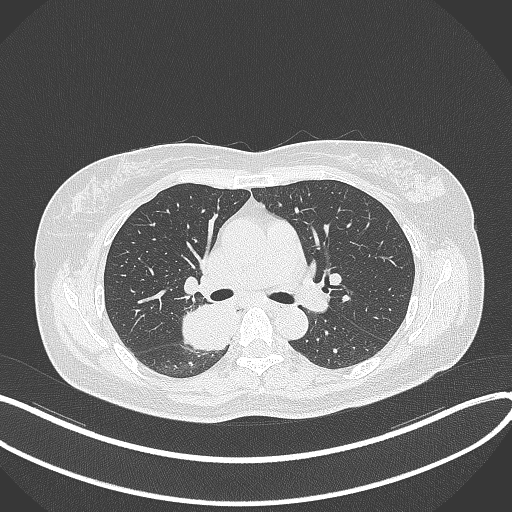
Chest CT, one axial slice; position 222 of 331 along the scan axis; lung window (W 1500 / L -600 HU); 1 mm slice thickness; 512 × 512 image matrix, field of view 400 × 400 mm. Female patient, age 54 years. Case-level facts recorded for this patient, not image findings: clinical TNM (as recorded): T4 N0 M0.
Outlined on this slice (bounding box drawn by a radiologist):
- lung tumour (recorded histology: adenocarcinoma): bounding box <181,303,238,354> (left, top, right, bottom; pixels)